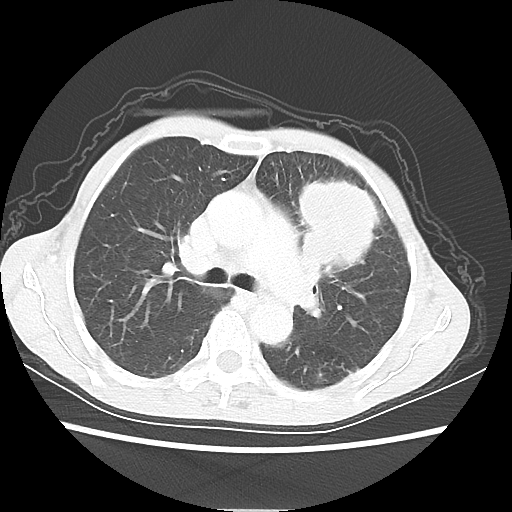
Chest CT, one axial slice; position 38 of 56 along the scan axis; reconstruction kernel LUNG; lung window (W 1500 / L -600 HU); 5 mm slice thickness; 512 × 512 image matrix, field of view 331 × 331 mm. Female patient, age 60 years. Case-level facts recorded for this patient, not image findings: clinical TNM (as recorded): T4 N1 M0.
Structures marked on this image (rectangle marked by the reading radiologist):
- lung tumour (recorded histology: adenocarcinoma): bounding box <292,170,389,278> (left, top, right, bottom; pixels)